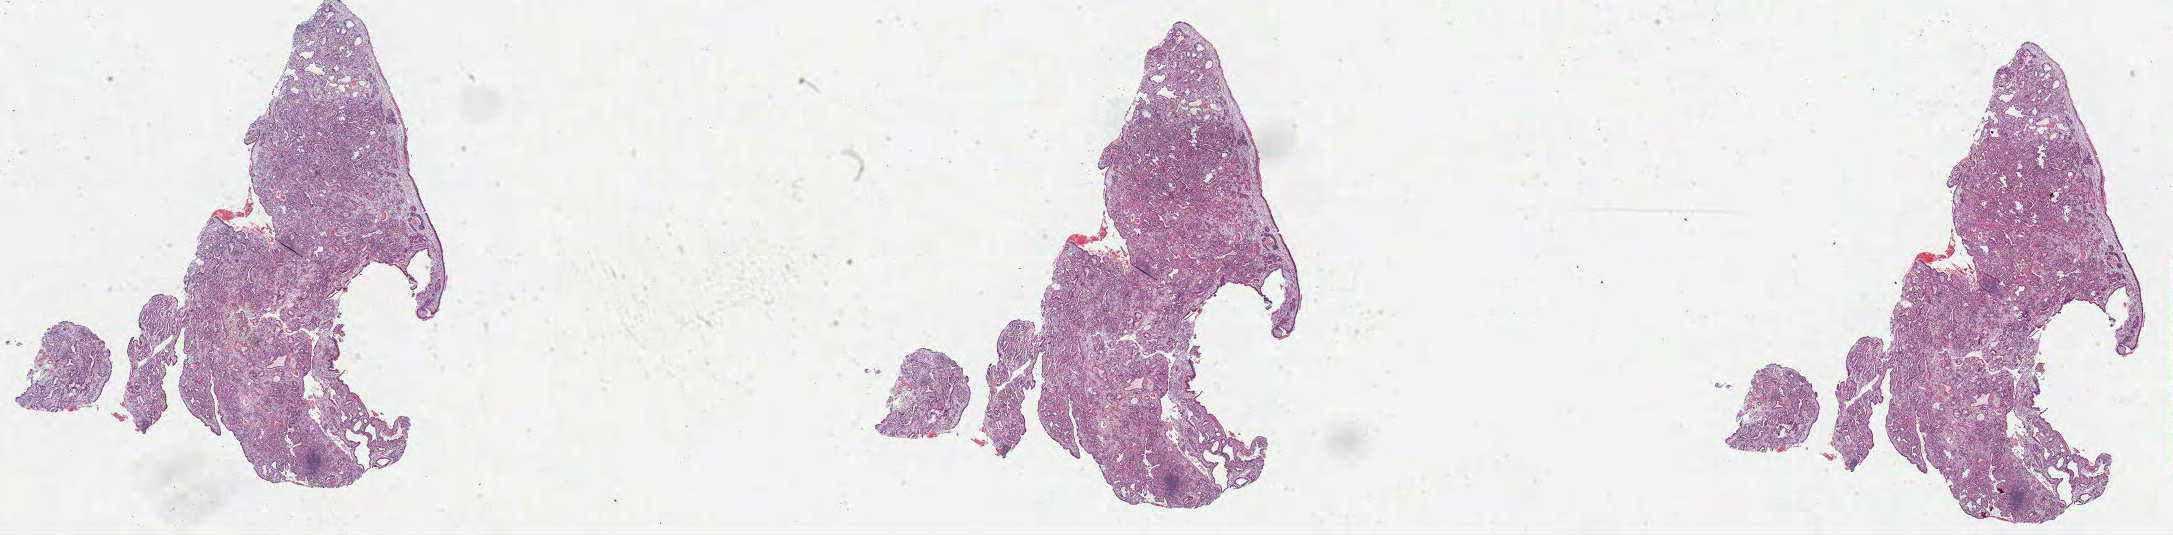
Whole-slide histology image, H&E — whole scanned area (about 35.1 x 8.6 mm, acquisition: 40x scan) shown as a low-resolution overview; formalin-fixed paraffin-embedded (FFPE) diagnostic section; sample: primary tumour, lung. Male, age 60 years at initial diagnosis.
- laterality: left
- pathologic diagnosis: Mucinous adenocarcinoma
- AJCC pathologic stage: IA (7th edition)